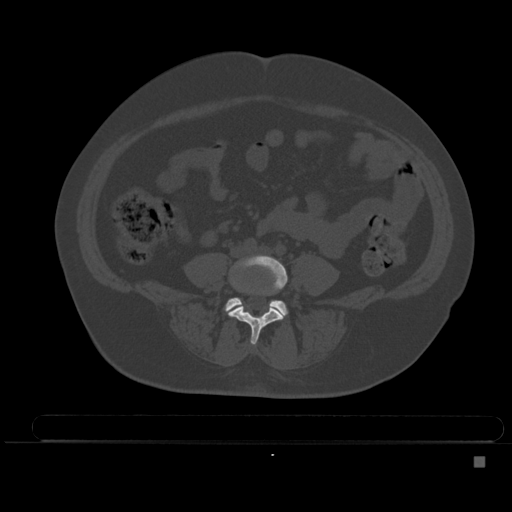
CT including the spine, one axial slice; slice 121 of 495 in the series (ordered by position); bone window (W 1800 / L 400 HU); 512 × 512 image matrix, field of view 404 × 404 mm. Female patient, age 33 years. From the clinical record (not read from this slice): primary cancer: breast; vertebrae with lytic lesions (as recorded): T1.
Annotated regions visible in this slice (semi-automatically segmented with operator editing):
- L4 vertebra: bounding box (x1, y1, x2, y2) in pixels: (228, 255, 288, 345)
- L5 vertebra: (225, 298, 287, 317)